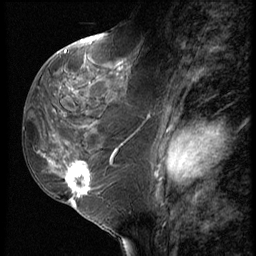
Breast MRI (dynamic contrast-enhanced), one sagittal slice. Position 30 of 62 along the scan axis. 3 images stored at this slice position (order not interpretable as contrast timing). 1.5 T. TE 4.2 ms, TR 9 ms. 2.5 mm slice thickness. 256 × 256 image matrix, field of view 180 × 180 mm. Patient: female, 50 years. From the clinical record (not read from this slice): setting: breast cancer imaged before/during neoadjuvant chemotherapy; receptor status: HR-positive, HER2-negative.
Outlined on this slice (semi-automatic segmentation, software-assisted and operator-edited):
- analysis volume of interest (the breast-tissue region the enhancement analysis was run in; not a lesion): bounding box <32,91,118,209> (left, top, right, bottom; pixels)
- tumour enhancement mask (voxels above the 140 % enhancement threshold inside the analysis volume of interest): <66,150,117,205>